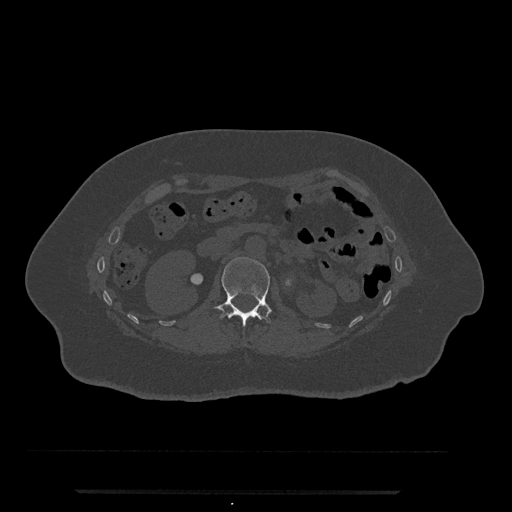
CT including the spine, one axial slice. Slice 102 of 797 in the series (ordered by position). Bone window (W 1800 / L 400 HU). 0.5 mm slice thickness. 512 × 512 image matrix, field of view 440 × 440 mm. Female patient, age 51 years. From the clinical record (not read from this slice): primary cancer: neuro.
Annotated regions visible in this slice (semi-automatic segmentation, software-assisted and operator-edited):
- L1 vertebra: bounding box [x1, y1, x2, y2] px = [213, 257, 272, 326]